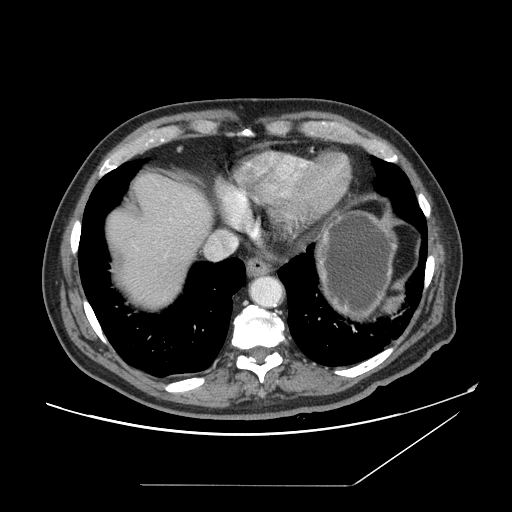
Contrast-enhanced abdominal CT, one axial slice. Position 138 of 166 along the scan axis. Intravenous contrast given. Soft-tissue window (W 400 / L 40 HU). 512 × 512 image matrix, field of view 416 × 416 mm. Male patient, age 80 years. From the clinical record (not read from this slice): diagnosis: colorectal cancer liver metastases, imaged before liver resection; multiple liver metastases: no; largest metastasis: 2.2 cm; disease in both lobes: no.
Structures marked on this image (outlined manually by an expert reader):
- hepatic veins: bounding box [x1, y1, x2, y2] px = [209, 236, 237, 258]
- liver: [105, 174, 214, 311]
- planned liver remnant (the part of the liver to remain after resection): [104, 174, 214, 257]